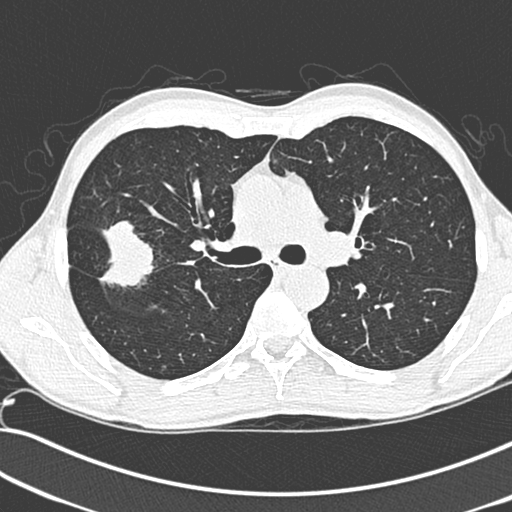
Low-dose screening chest CT, one axial slice. Slice 191 of 281 in the series (ordered by position). 120 kVp. Lung window (W 1500 / L -600 HU). 1.3 mm slice thickness. 512 × 512 image matrix, field of view 341 × 341 mm.
Annotated regions visible in this slice (manually delineated by an expert):
- lesion 1 (tumor, upper lobe of right lung): bounding box (x1, y1, x2, y2) in pixels: (99, 221, 155, 287)